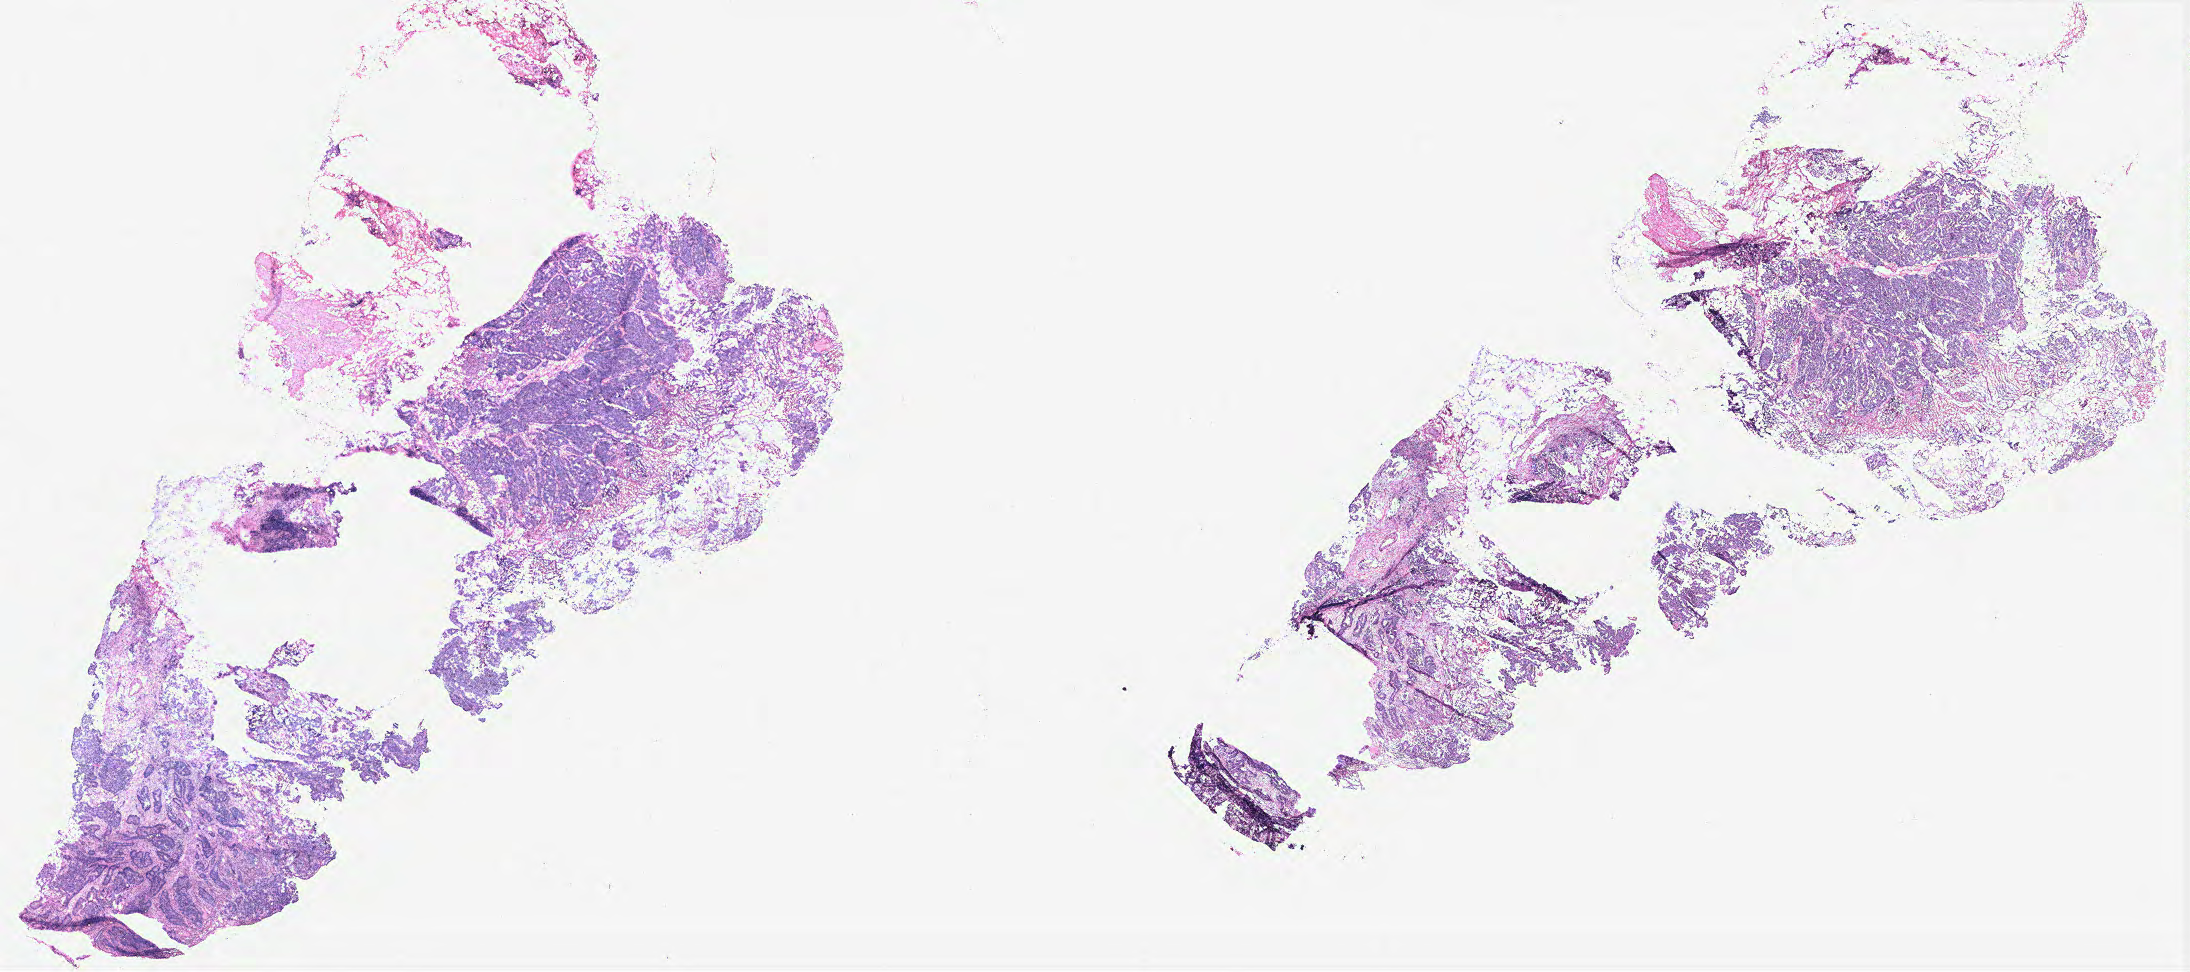
Digitized Hematoxylin and eosin (H&E) stained tissue section (whole slide), low-resolution overview of the scanned area, about 35.1 x 15.6 mm (acquisition: 40x scan); normal (non-tumour) tissue sample, colon. 75-year-old female patient.
This section: normal (non-tumour) tissue from the same patient. Patient diagnosis: Adenocarcinoma, NOS.